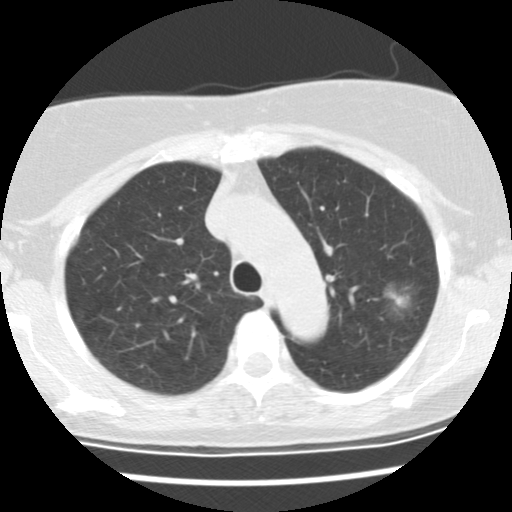
Low-dose screening chest CT, axial slice. First (baseline) screen. Lung window (W 1500 / L -600 HU). 2.5 mm slice thickness. Slice 104 of 137 in the series. Female participant, aged 66 years at enrolment.
- Expert reader's lesion annotation, bounding box <377,278,427,324> (left, top, right, bottom; pixels).
- Reader record for this screening exam (exam-level; its link to the box is not recorded): non-calcified nodule or mass ≥4 mm, left upper lobe, 25 × 17 mm, poorly defined margins, mixed attenuation.
- Later outcome: lung cancer diagnosed 44 days after this screen — bronchiolo-alveolar adenocarcinoma, NOS, left upper lobe, well differentiated (G1), stage IA (AJCC 6th edition), 19 mm at pathology.